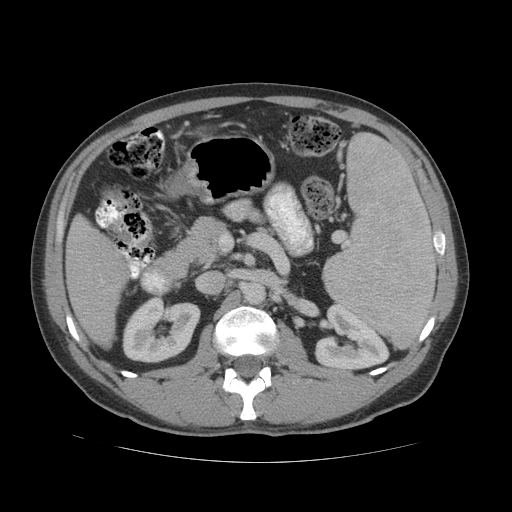
Contrast-enhanced abdominal CT (liver protocol), one axial slice; slice 20 of 81 in the series (ordered by position); soft-tissue window (W 400 / L 40 HU); 2.5 mm slice thickness; 512 × 512 image matrix, field of view 400 × 400 mm. Case-level facts recorded for this patient, not image findings: diagnosis: hepatocellular carcinoma (patient treated with transarterial chemoembolisation; whether this scan precedes or follows treatment is not stated here); TNM stage (as recorded): Stage-IVB; Child-Pugh class: B; tumour differentiation: well differentiated; tumour nodularity: multinodular.
Structures marked on this image (semi-automatic segmentation, software-assisted and operator-edited):
- liver parenchyma outside the tumour (the mass and vessels are separate outlines, so this box may not span the whole liver): box from (x=66, y=214) to (x=128, y=346) px